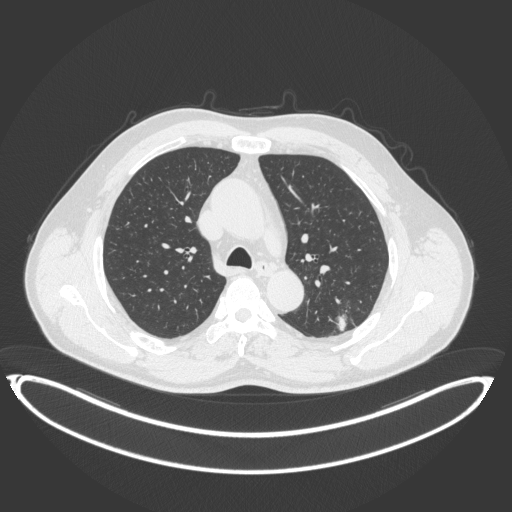
Chest CT, one axial slice. Reconstruction kernel B31f. Lung window (W 1500 / L -600 HU). 1 mm slice thickness. 512 × 512 image matrix. Patient: male, 58 years. From the clinical record (not read from this slice): clinical TNM (as recorded): T1c N0 M0.
Outlined on this slice (bounding box drawn by a radiologist):
- lung tumour (recorded histology: adenocarcinoma): bounding box [x1, y1, x2, y2] px = [327, 310, 359, 339]